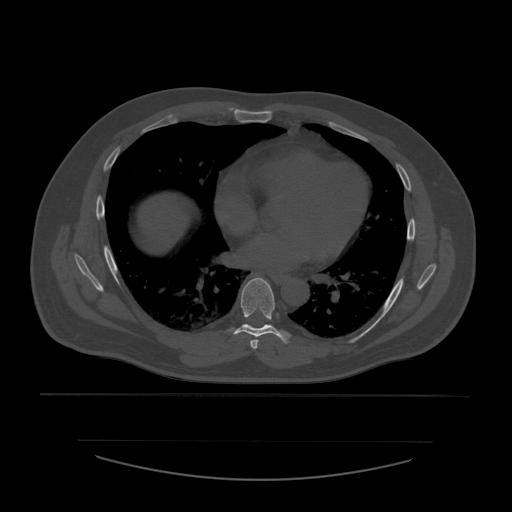
CT including the spine, one axial slice. Position 360 of 532 along the scan axis. Reconstruction kernel STANDARD. 120 kVp. Bone window (W 1800 / L 400 HU). 1.25 mm slice thickness. 512 × 512 image matrix, field of view 441 × 441 mm. Patient age 44 years. Case-level facts recorded for this patient, not image findings: primary cancer: soft tissue sarcoma.
Outlined on this slice (semi-automatic segmentation, software-assisted and operator-edited):
- T6 vertebra: bounding box [x1, y1, x2, y2] px = [250, 340, 259, 350]
- T7 vertebra: [231, 278, 291, 344]